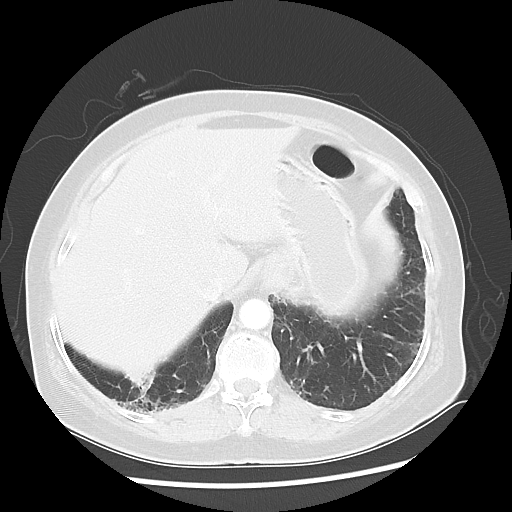
Chest CT, one axial slice; position 11 of 56 along the scan axis; 120 kVp; lung window (W 1500 / L -600 HU); 512 × 512 image matrix, field of view 360 × 360 mm. Patient: female, 64 years. Case-level facts recorded for this patient, not image findings: clinical TNM (as recorded): Tis N0 M0.
Structures marked on this image (rectangle marked by the reading radiologist):
- lung tumour (recorded histology: adenocarcinoma): box from (x=112, y=362) to (x=181, y=428) px